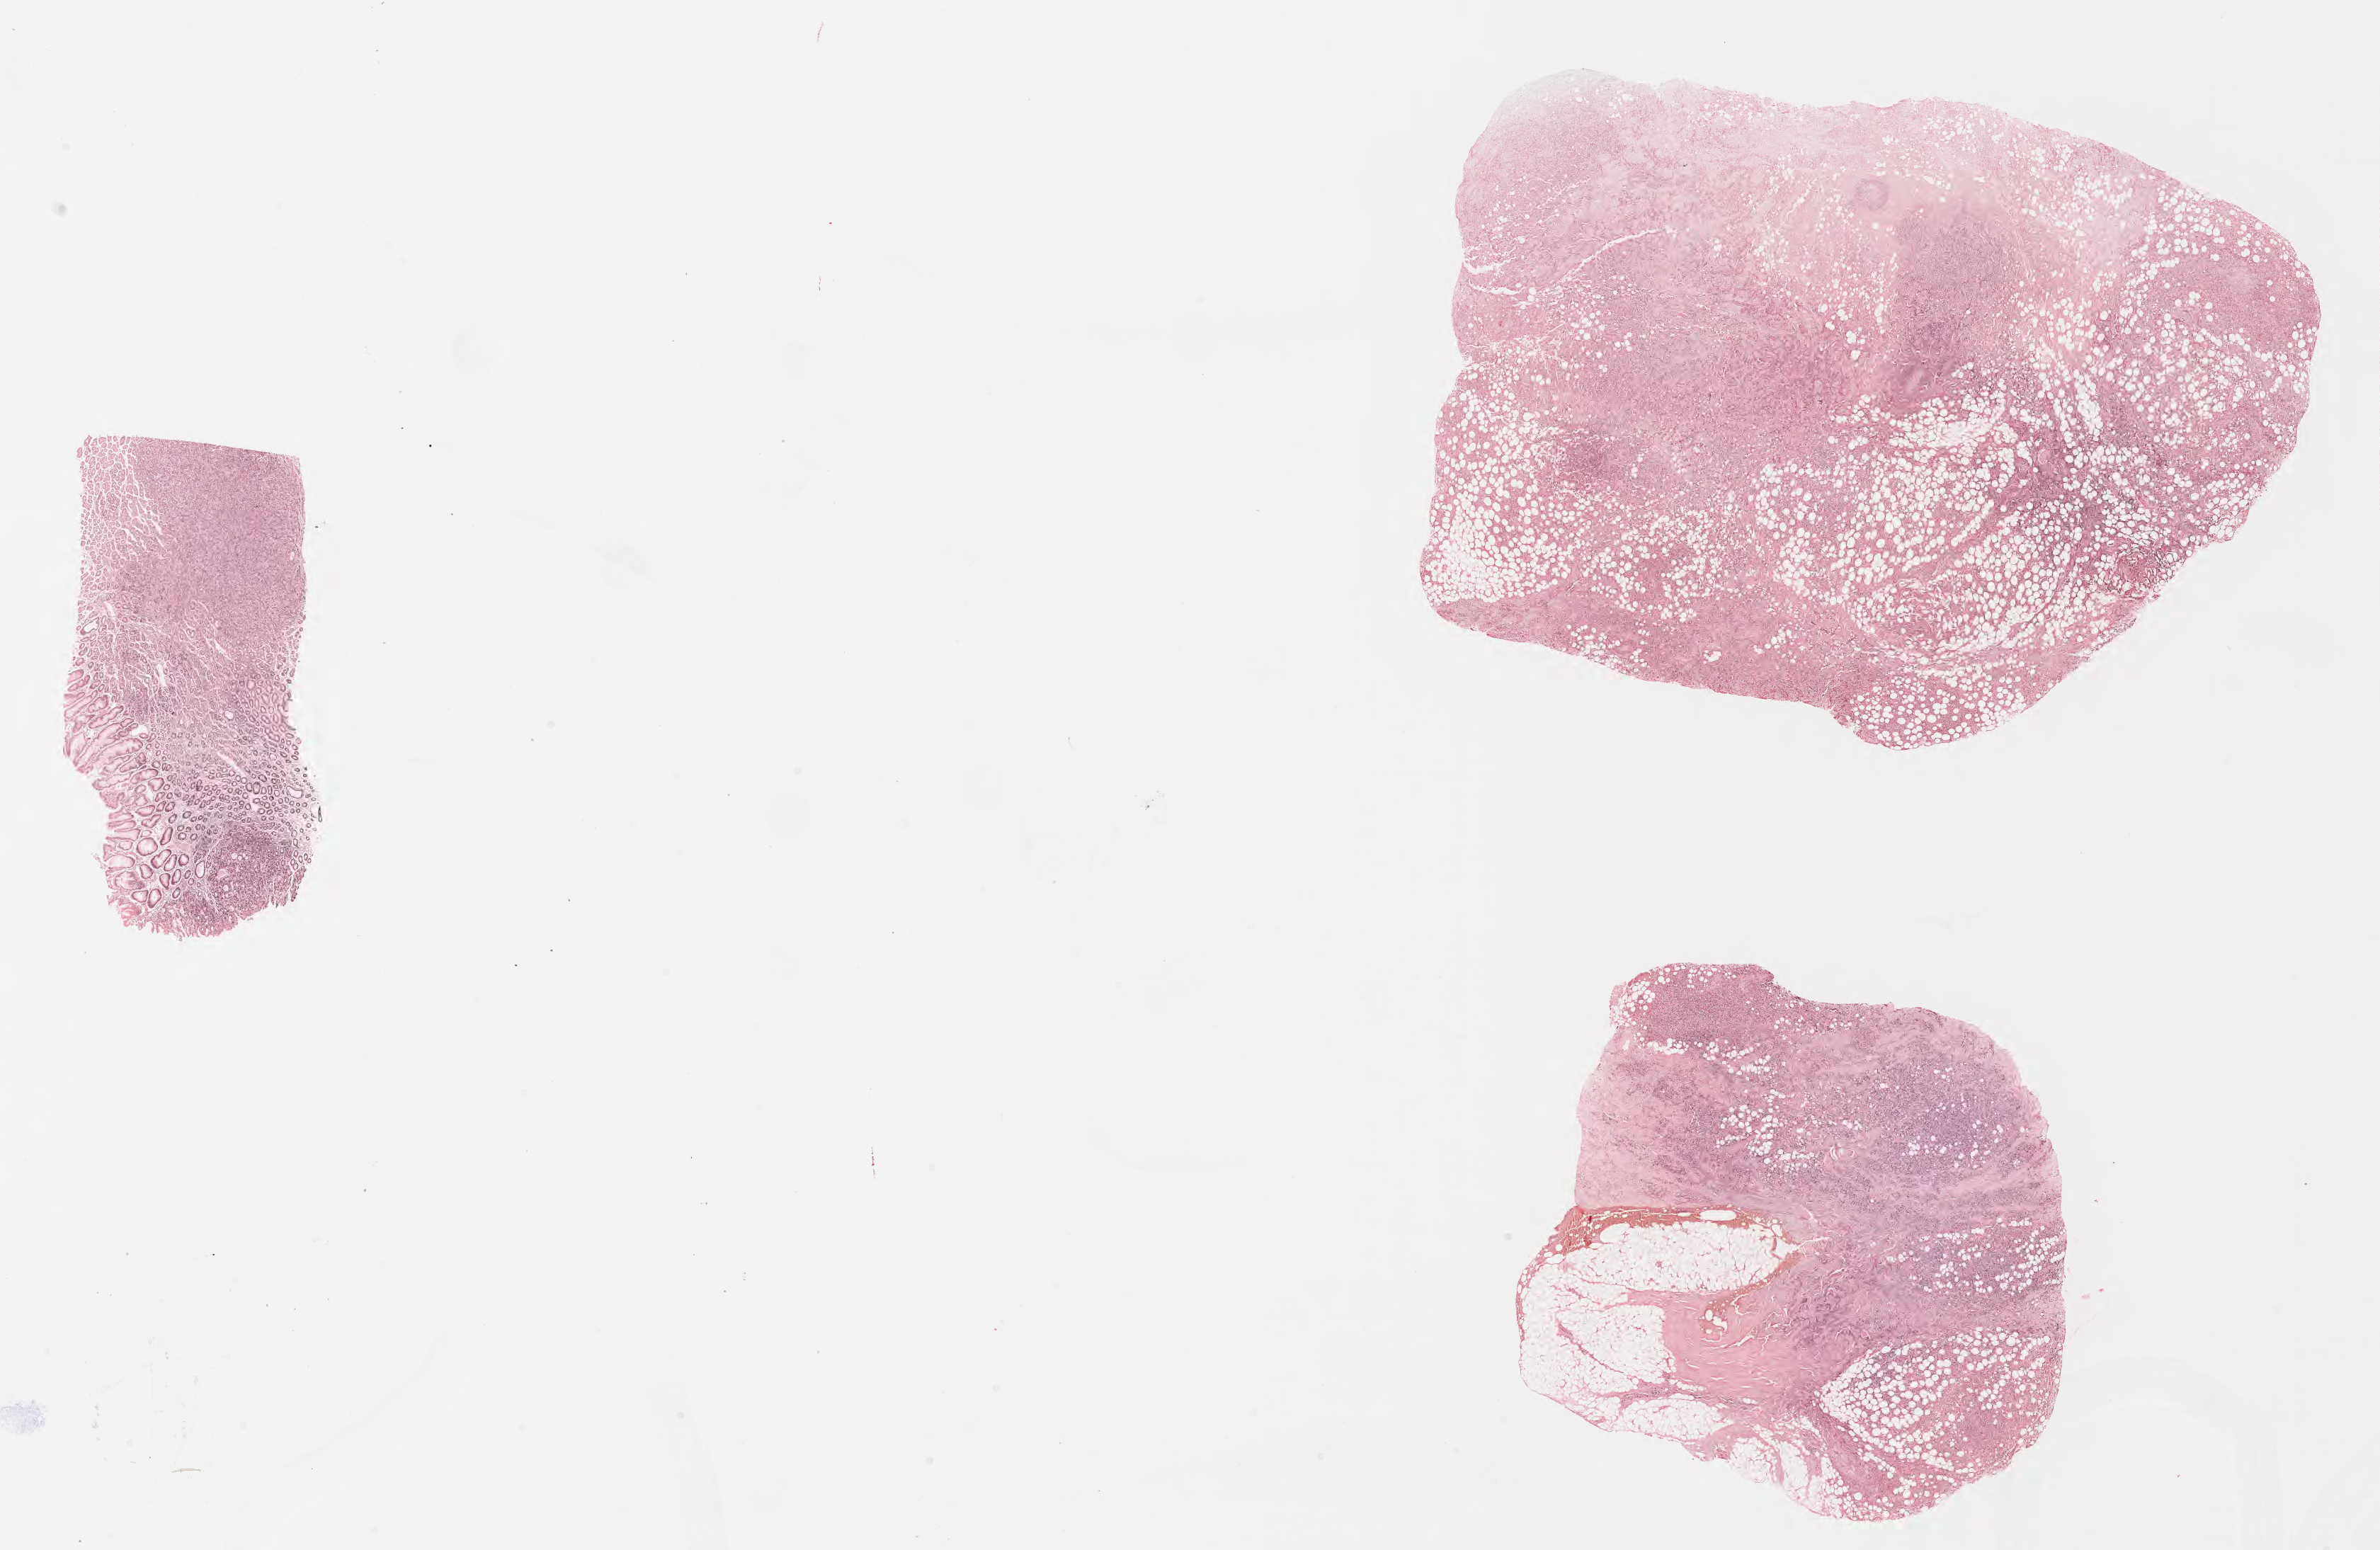
Whole-slide image; stain recorded as Iodonitrotetrazolium — whole scanned area (about 27.2 x 17.7 mm) shown as a low-resolution overview; tumor tissue; anatomic site: kidney. Patient male; age 63 years.
* diagnosis: Diffuse large B-cell lymphoma, NOS